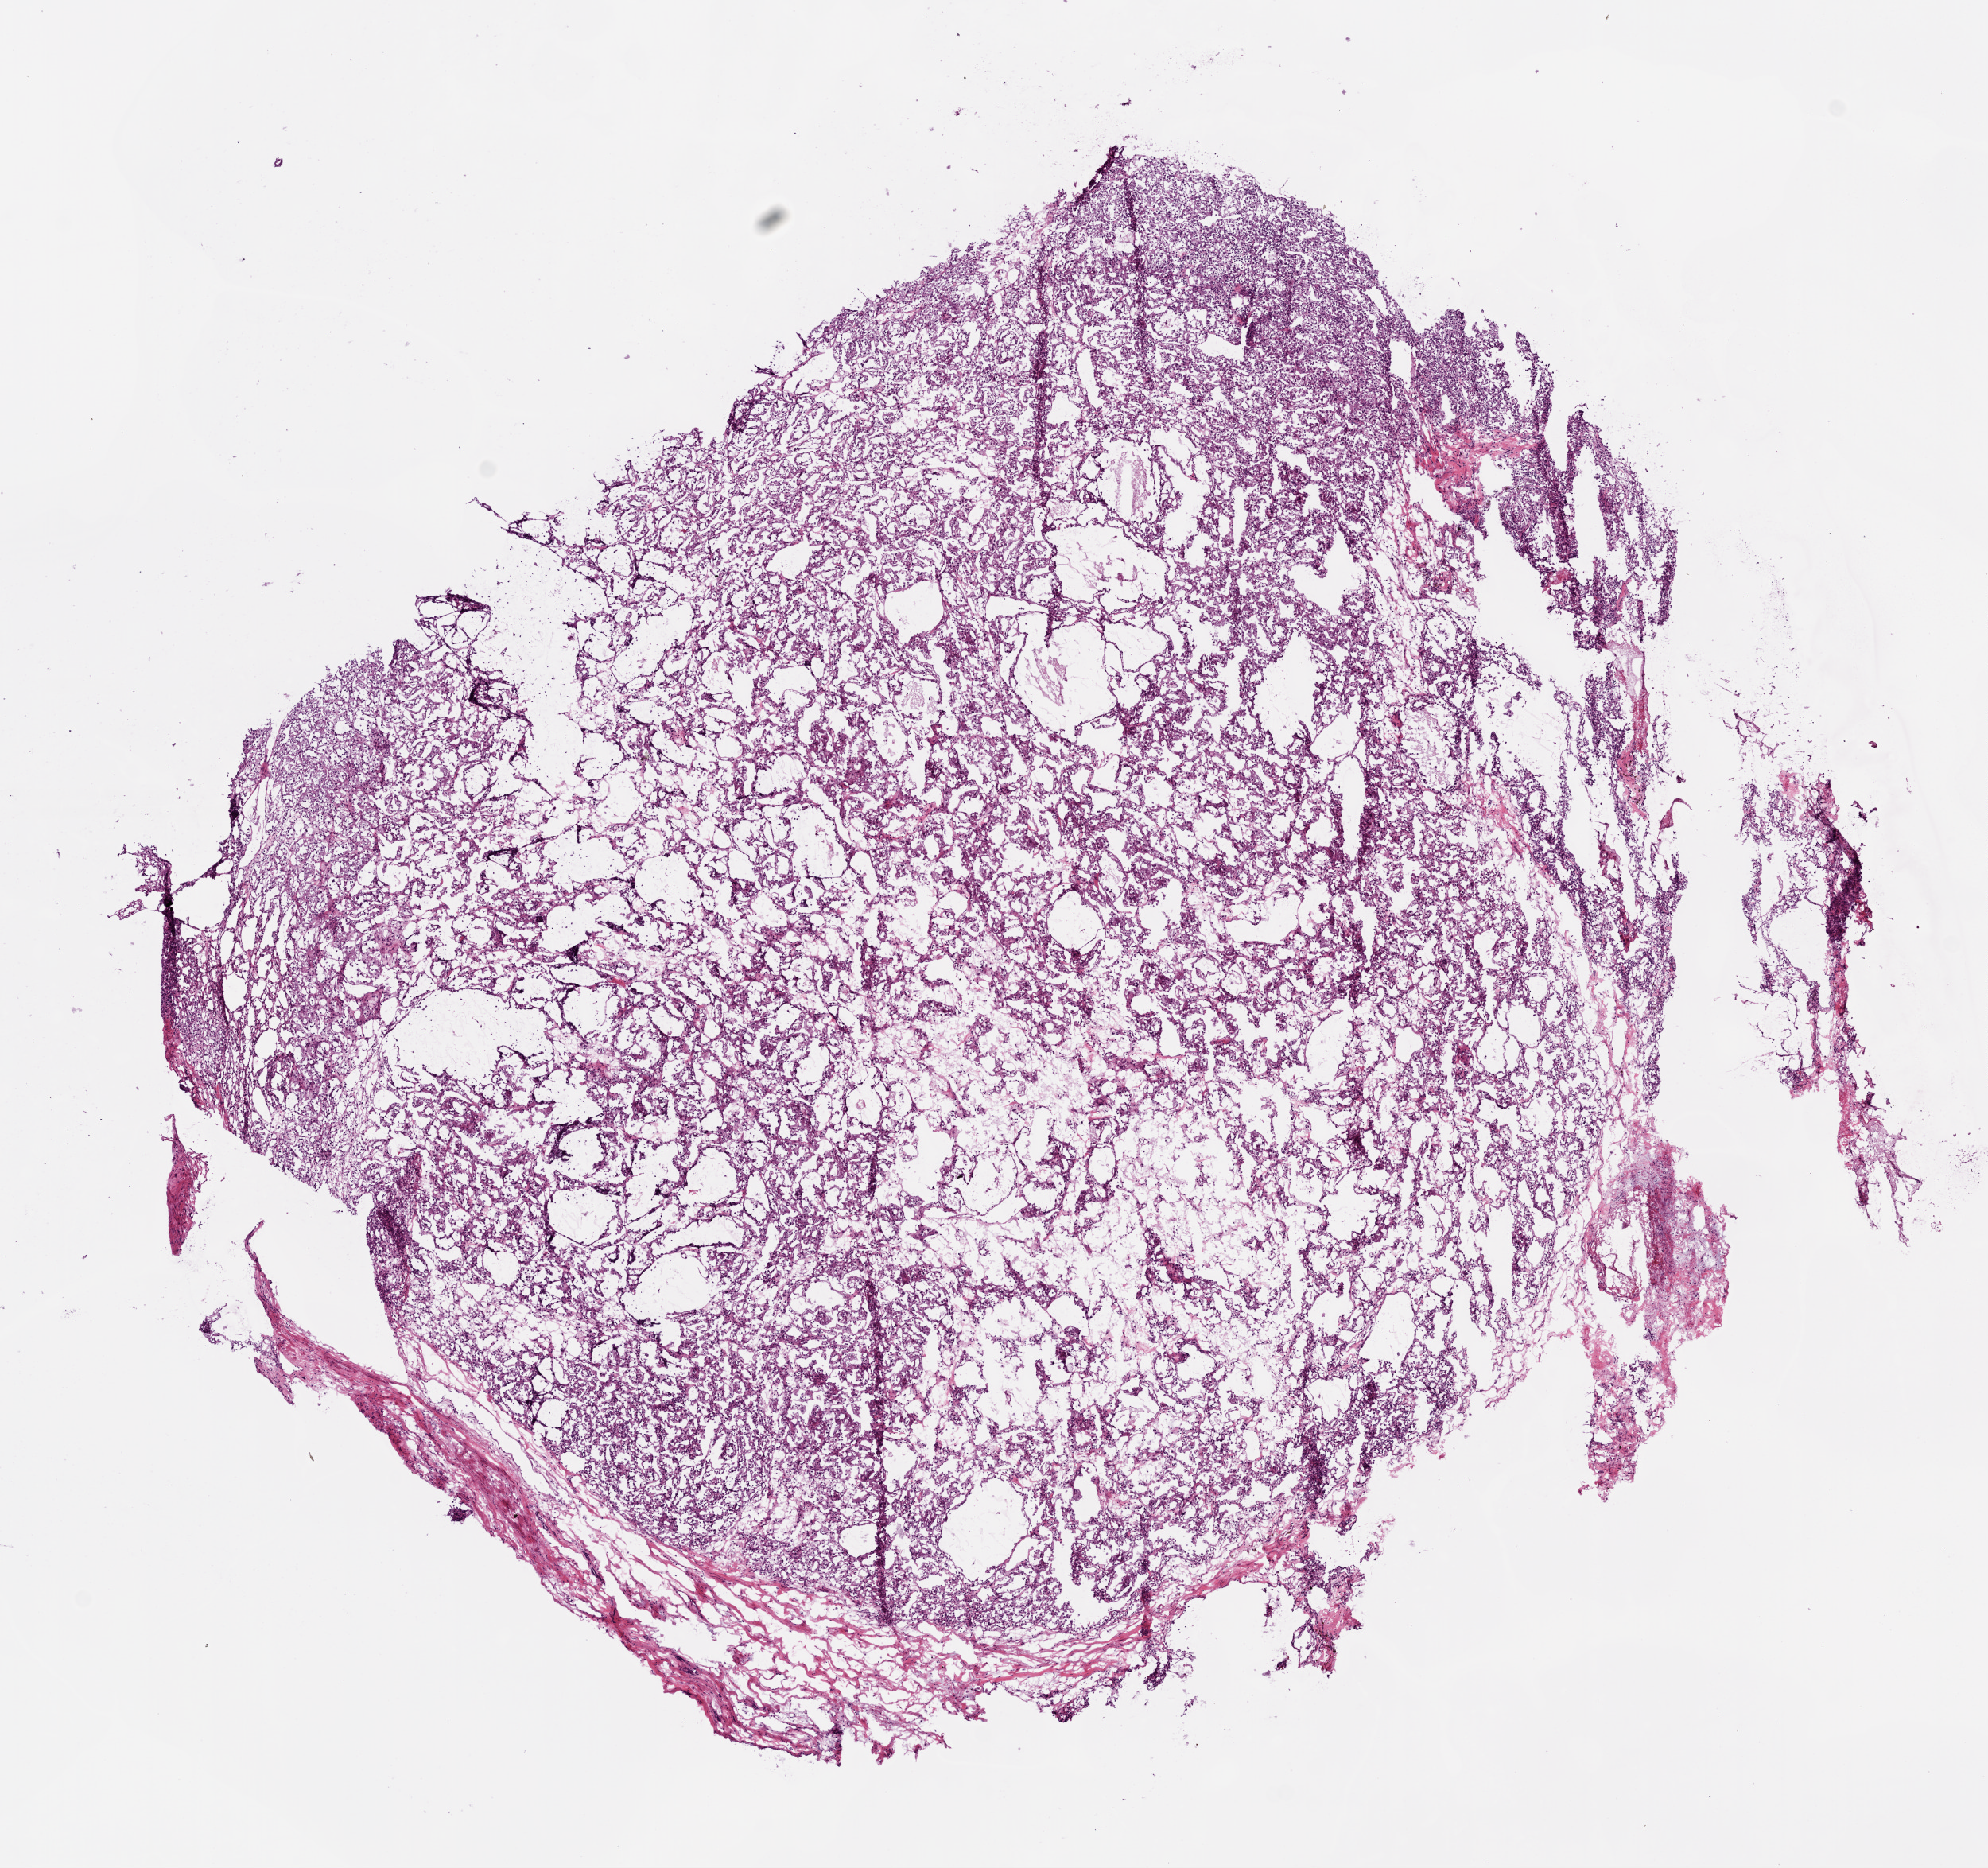
Whole-slide histology image, H&E — shown as a low-resolution overview of the whole scanned area (about 10.0 x 9.4 mm). Frozen section from the top of the tissue portion. Primary tumour sample from the kidney. Male, age 71 years at initial diagnosis.
Histologic diagnosis: Clear cell adenocarcinoma, NOS.